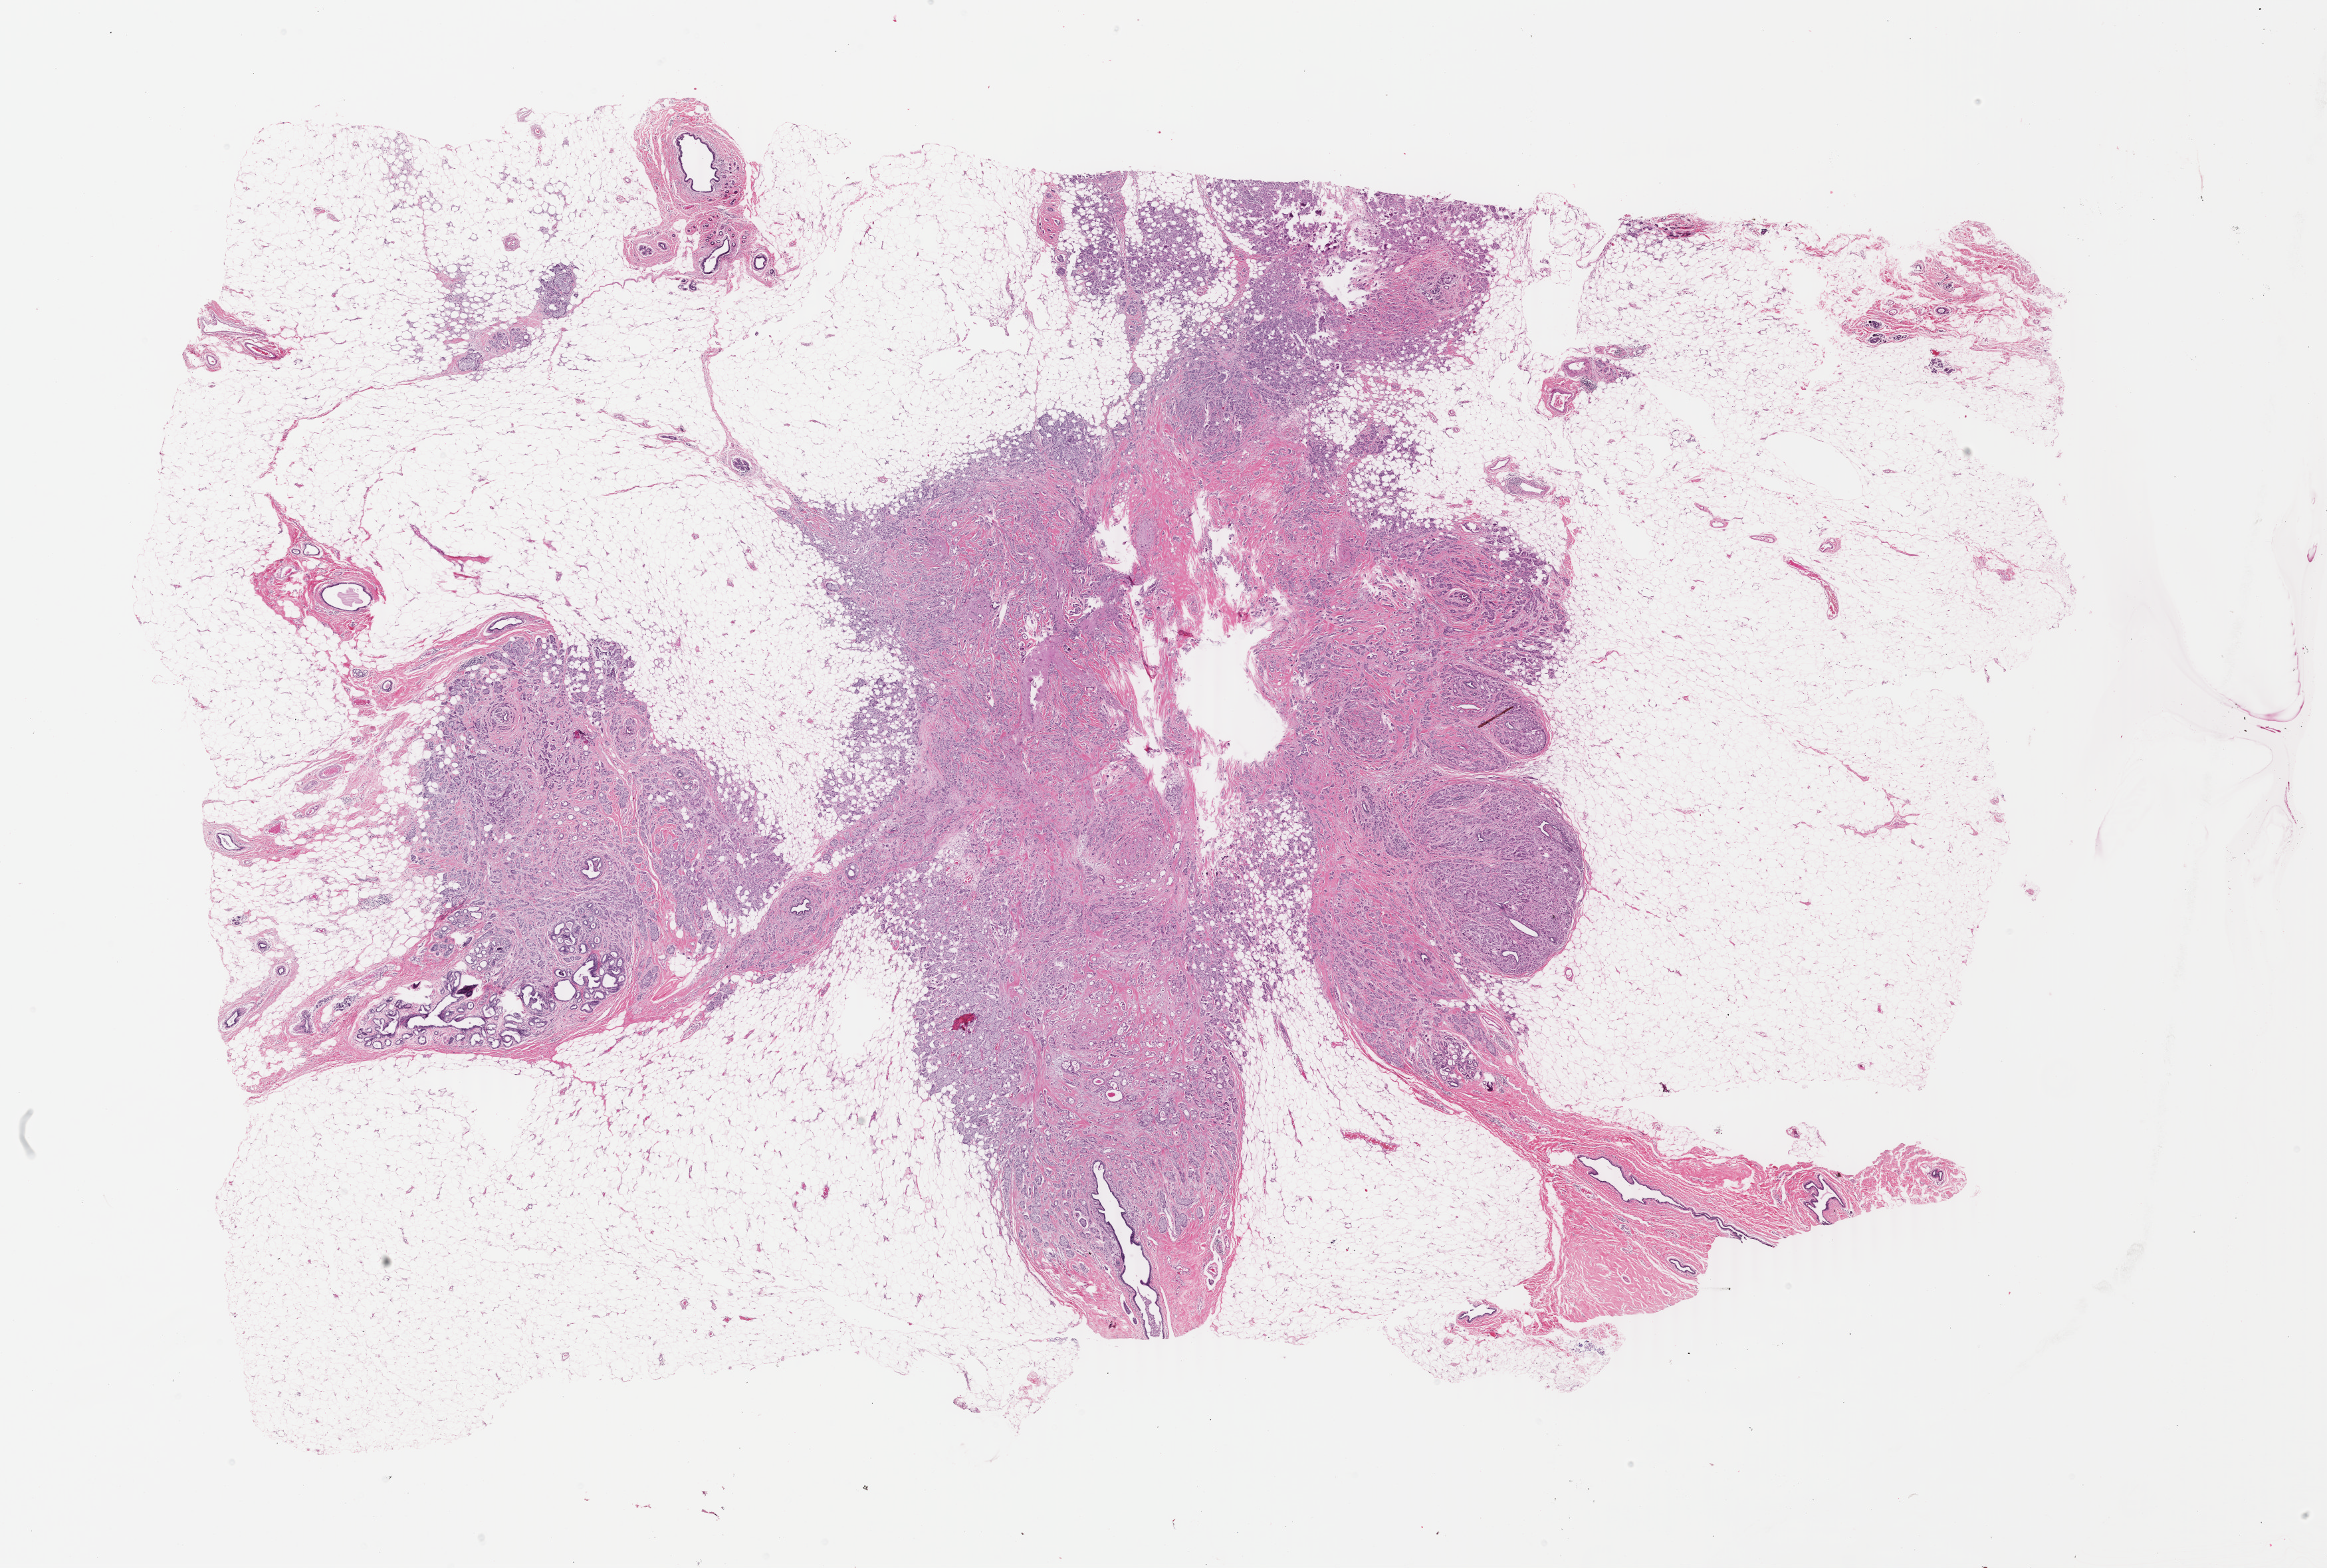
Whole-slide histology image, H&E — shown as a low-resolution overview of the whole scanned area (about 27.8 x 18.8 mm, from a 40x scan). FFPE section. Breast, primary tumour sample. Female, age 50 years at initial diagnosis.
Laterality: right. AJCC pathologic stage: II (4th edition). Lymph nodes positive (case pathology): 11 of 21 examined. Diagnosis: Infiltrating duct carcinoma, NOS.